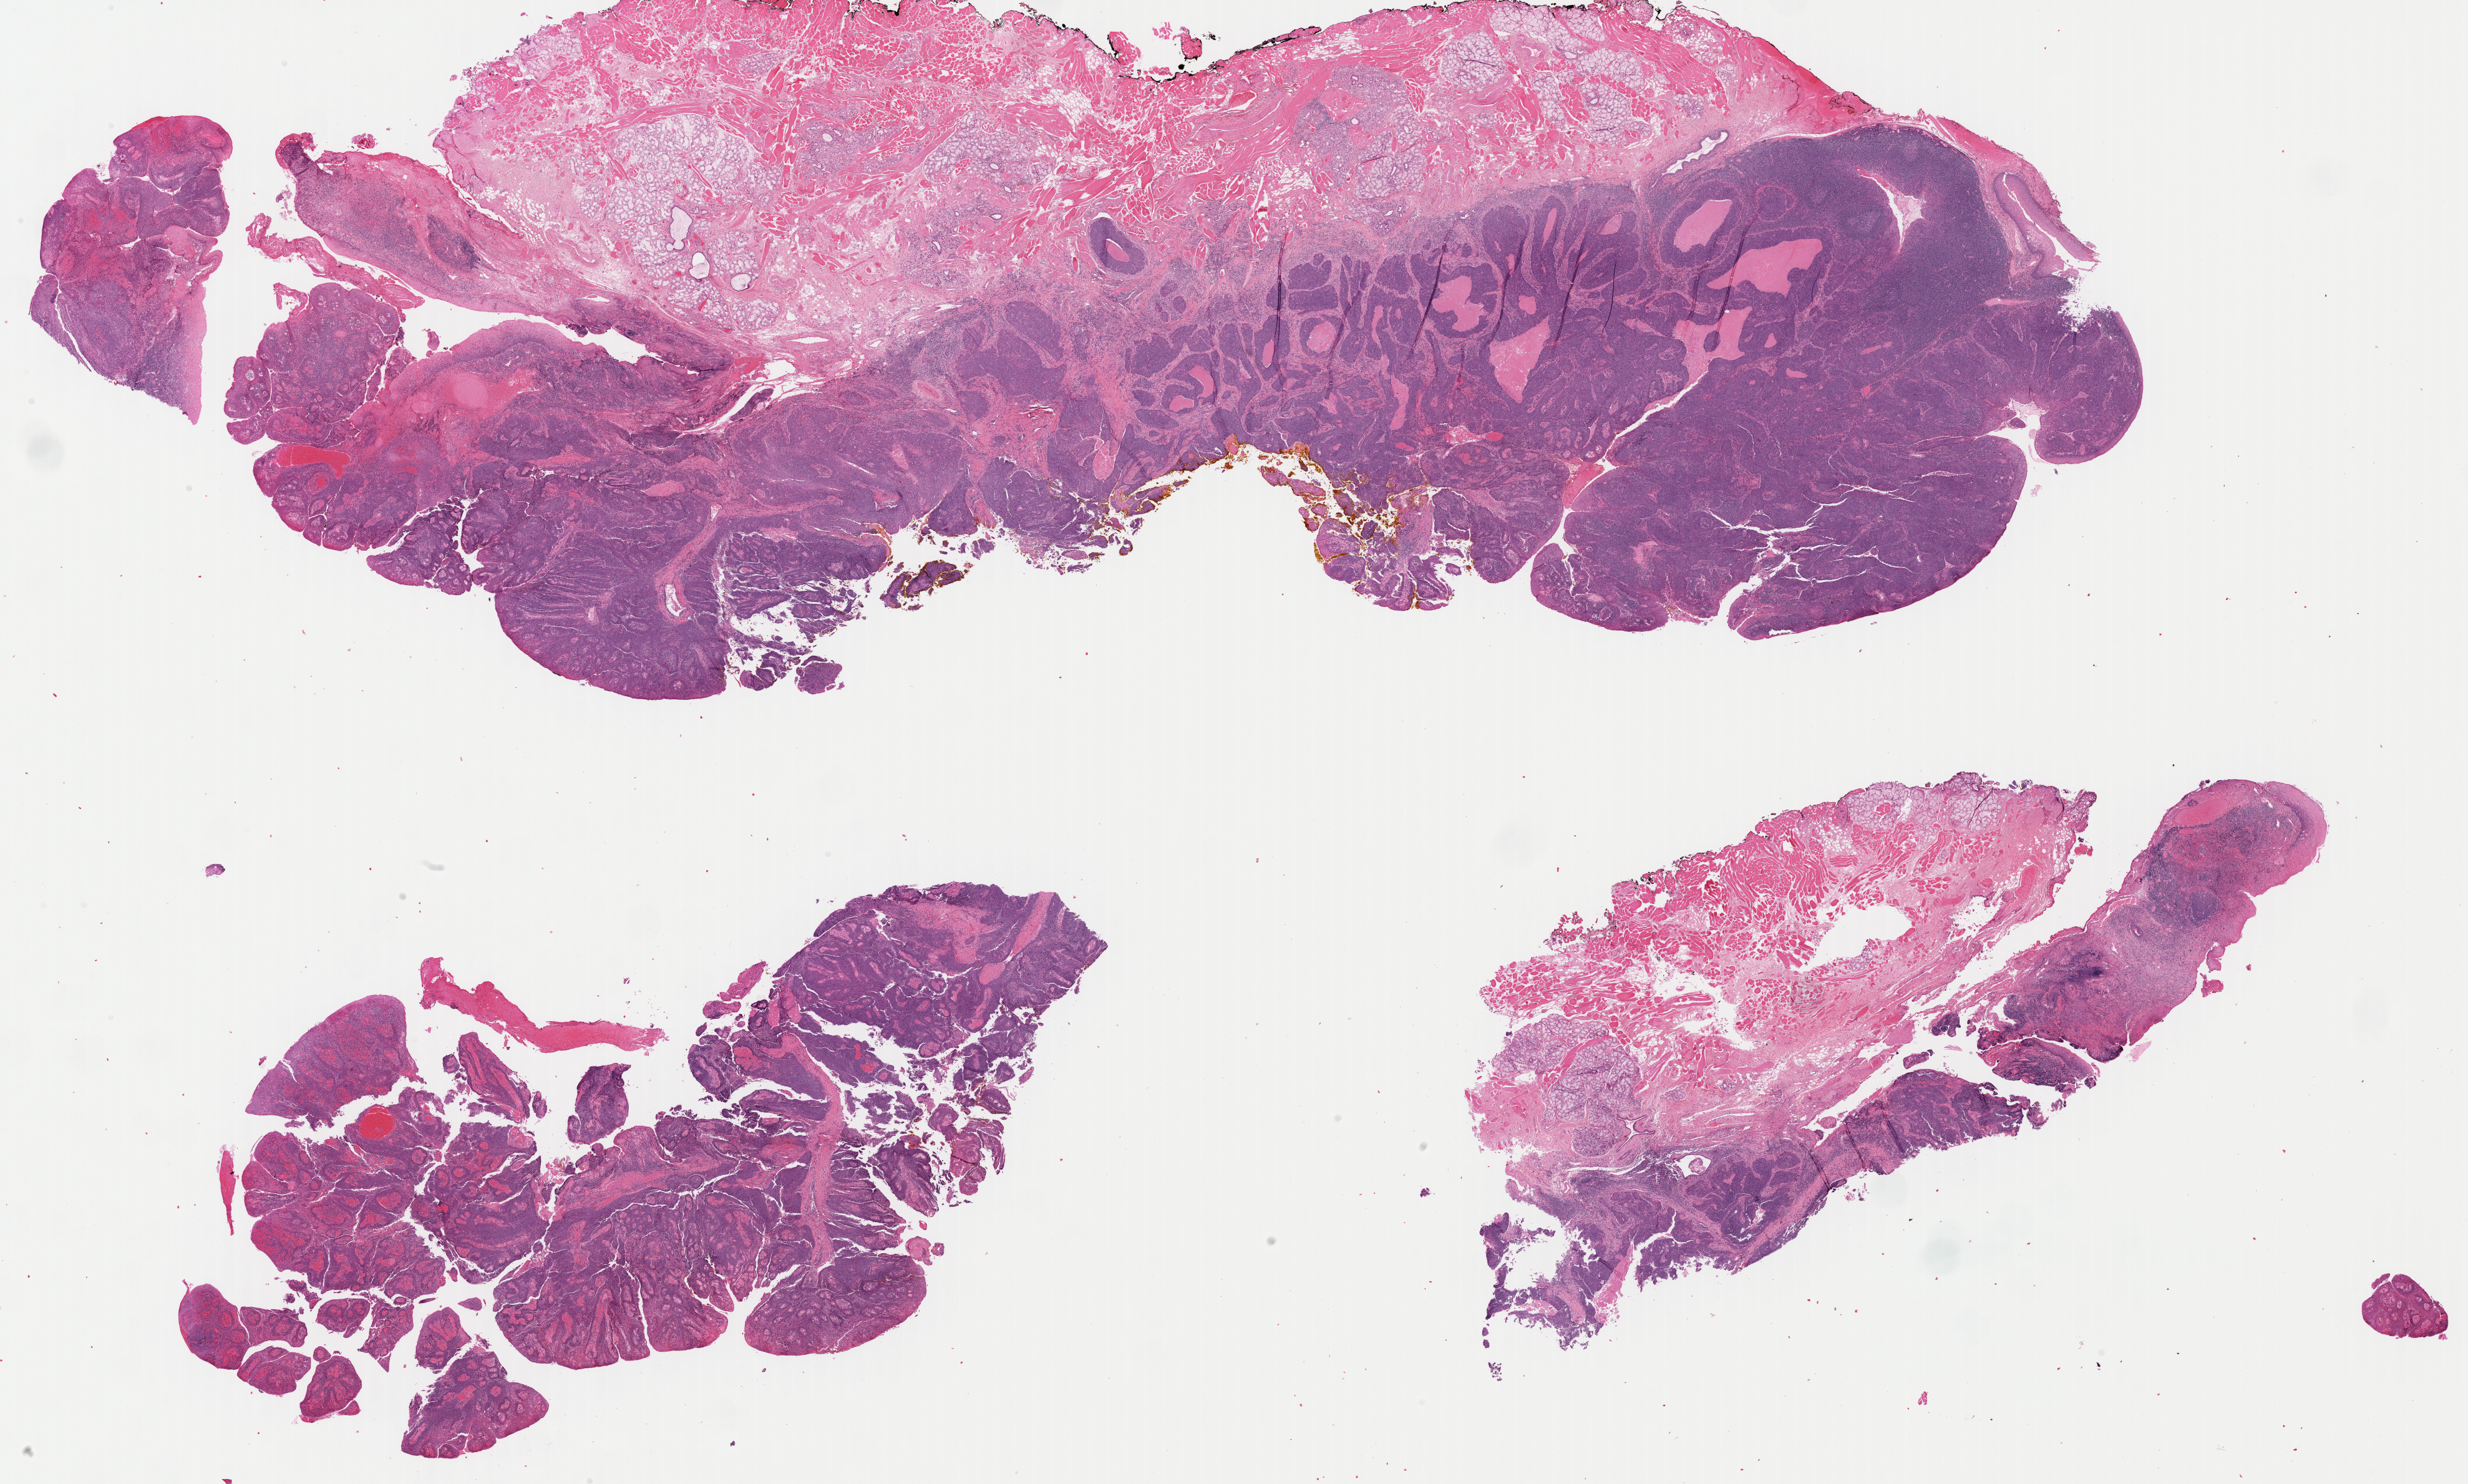
Digitized H&E-stained tissue section (whole slide), whole scanned area (about 31.2 x 18.8 mm, from a 40x scan) shown as a low-resolution overview. Formalin-fixed paraffin-embedded (FFPE) diagnostic section. Head and neck, primary tumour sample. Patient: male, age at initial diagnosis 49 years.
Histologic diagnosis: Basaloid squamous cell carcinoma (base of tongue, NOS).